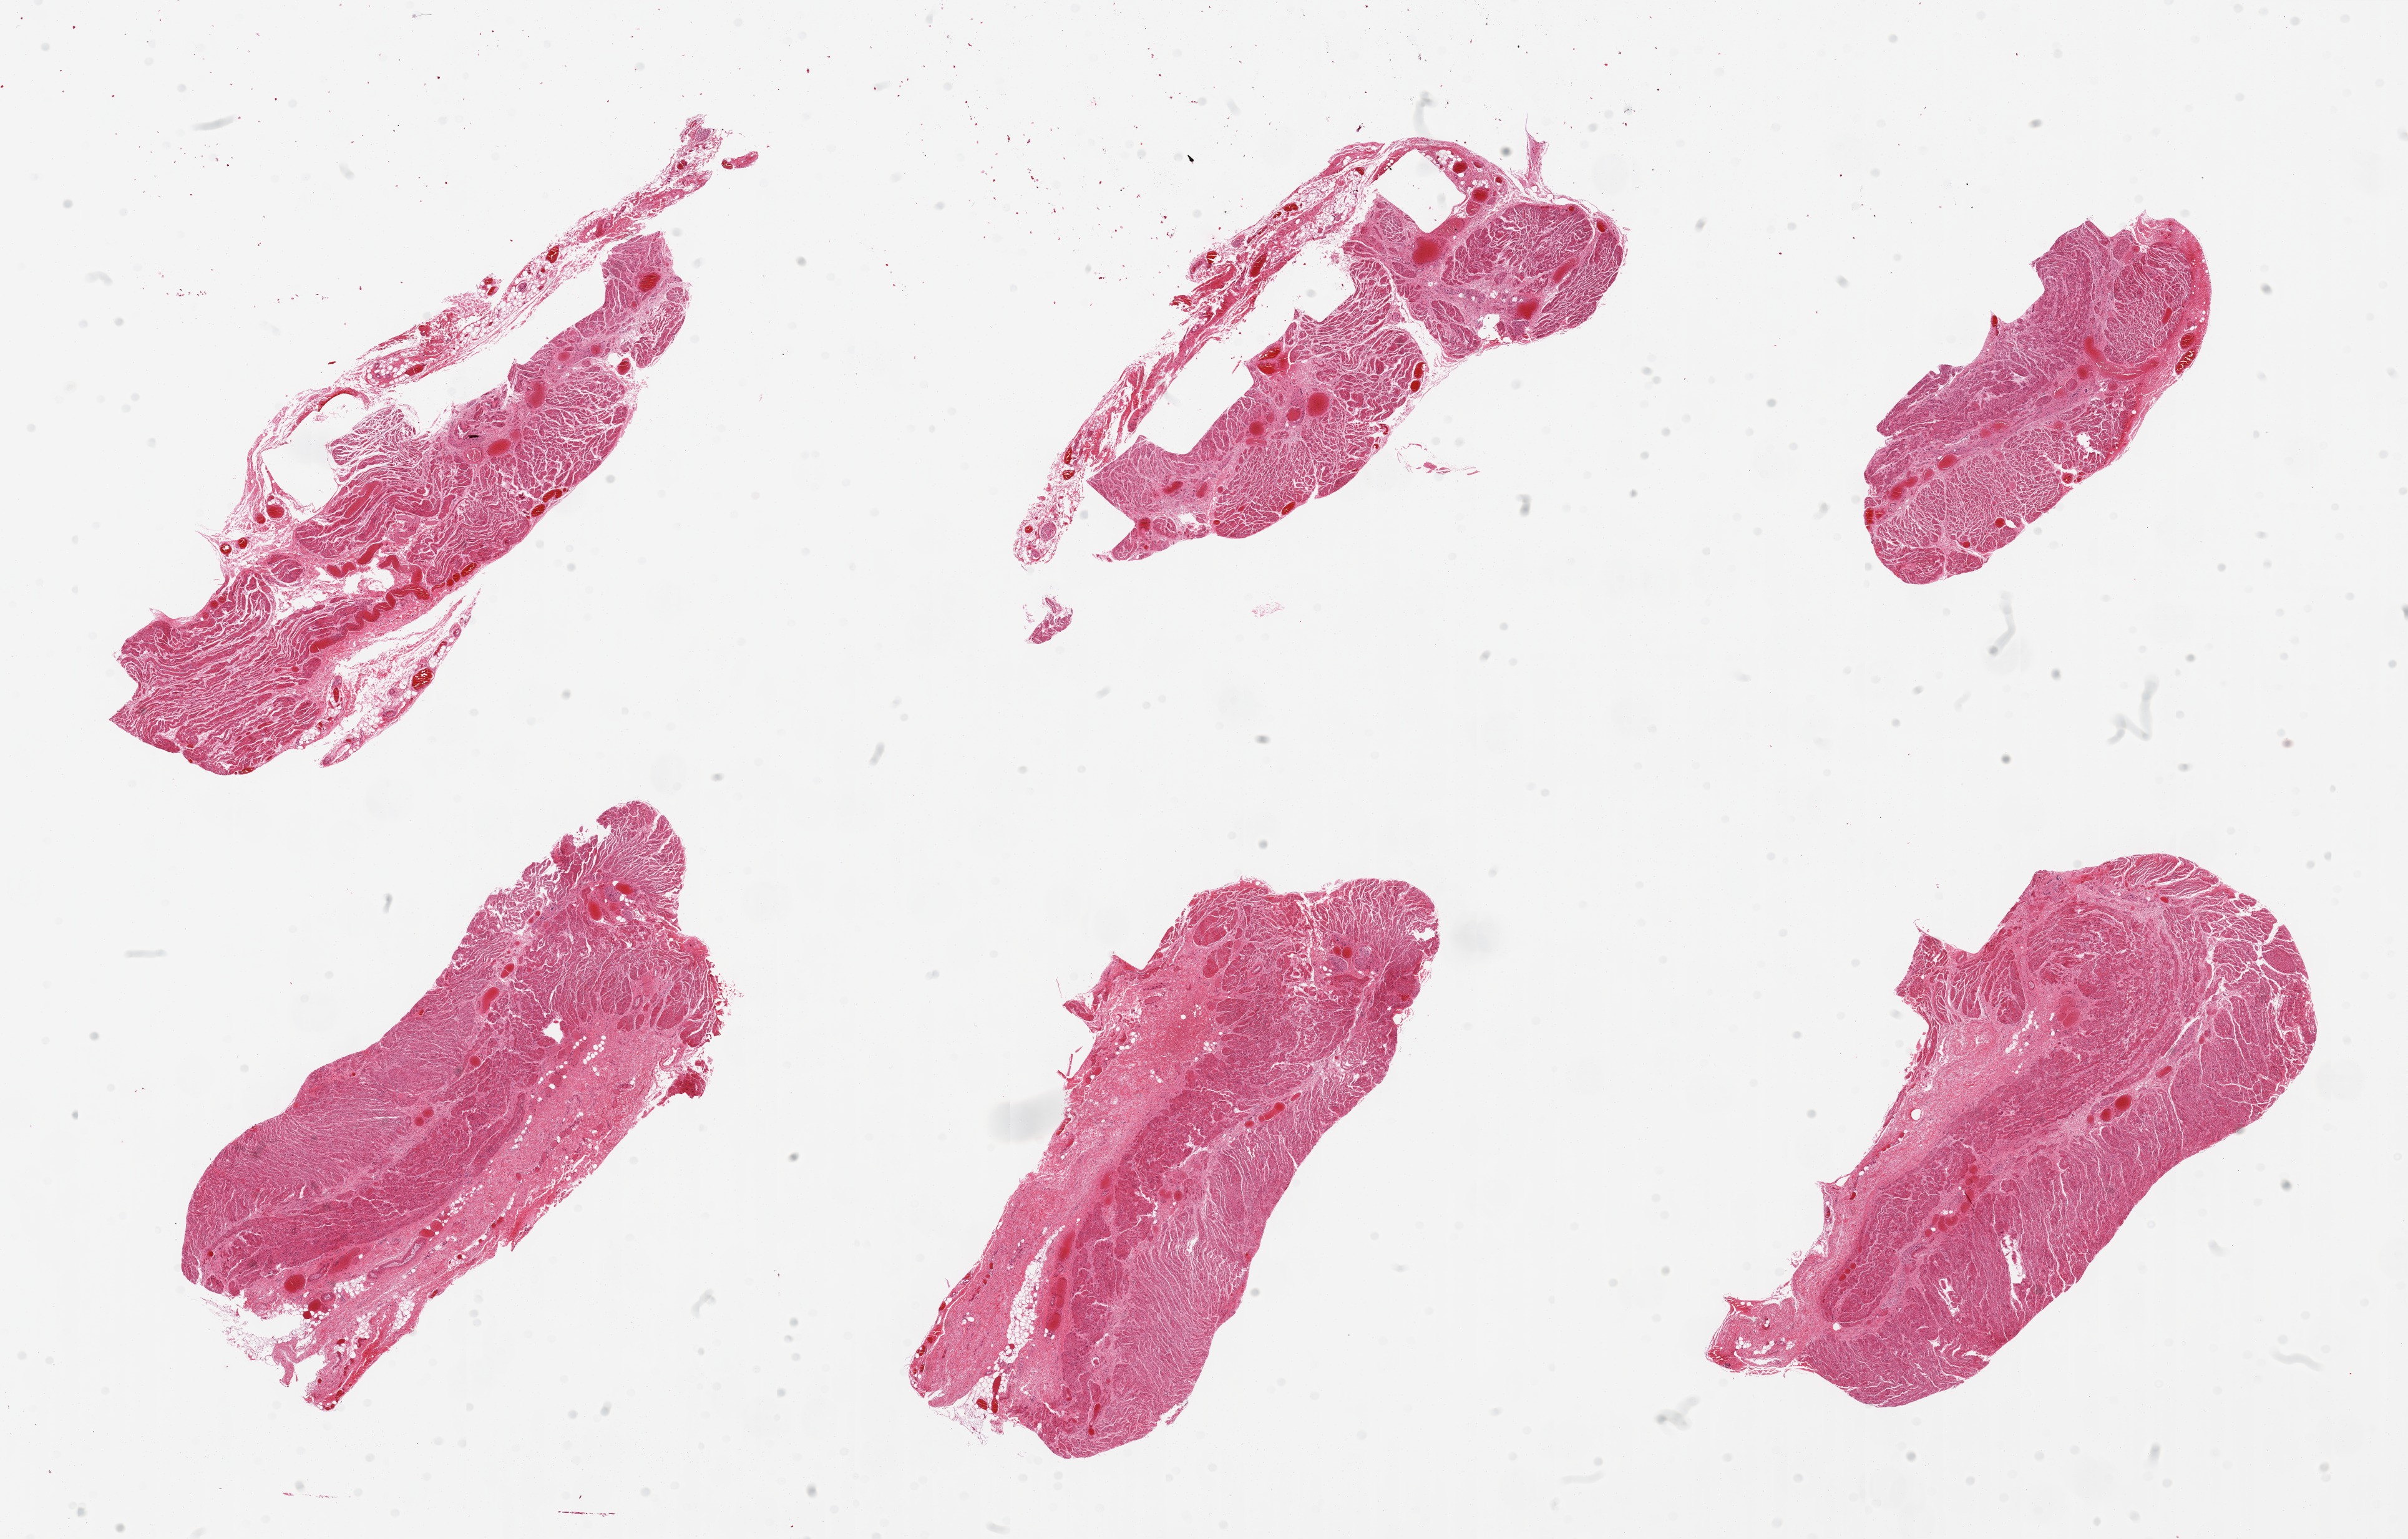
Whole-slide image, hematoxylin and eosin (H&E) stain, whole scanned area (about 30.5 x 19.5 mm) shown as a low-resolution overview. PAXgene-fixed, paraffin-embedded tissue. Section of gastroesophageal junction (target tissue). Donor tissue sample.
Review note (as recorded): 6 pieces, well trimmed muscle.